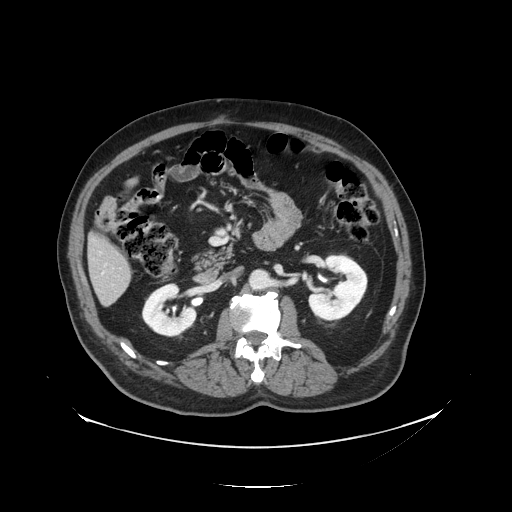
Contrast-enhanced abdominal CT, one axial slice. Position 48 of 138 along the scan axis. Reconstruction kernel STANDARD. 120 kVp. Intravenous contrast given. Soft-tissue window (W 400 / L 40 HU). 2.5 mm slice thickness. 512 × 512 image matrix, field of view 497 × 497 mm. Male patient, age 77 years. From the clinical record (not read from this slice): diagnosis: colorectal cancer liver metastases, imaged before liver resection; multiple liver metastases: no; largest metastasis: 1.5 cm; disease in both lobes: no.
Structures marked on this image (manually delineated by an expert):
- liver: box from (x=89, y=238) to (x=132, y=306) px
- planned liver remnant (the part of the liver to remain after resection): (x=89, y=238)–(x=130, y=279)